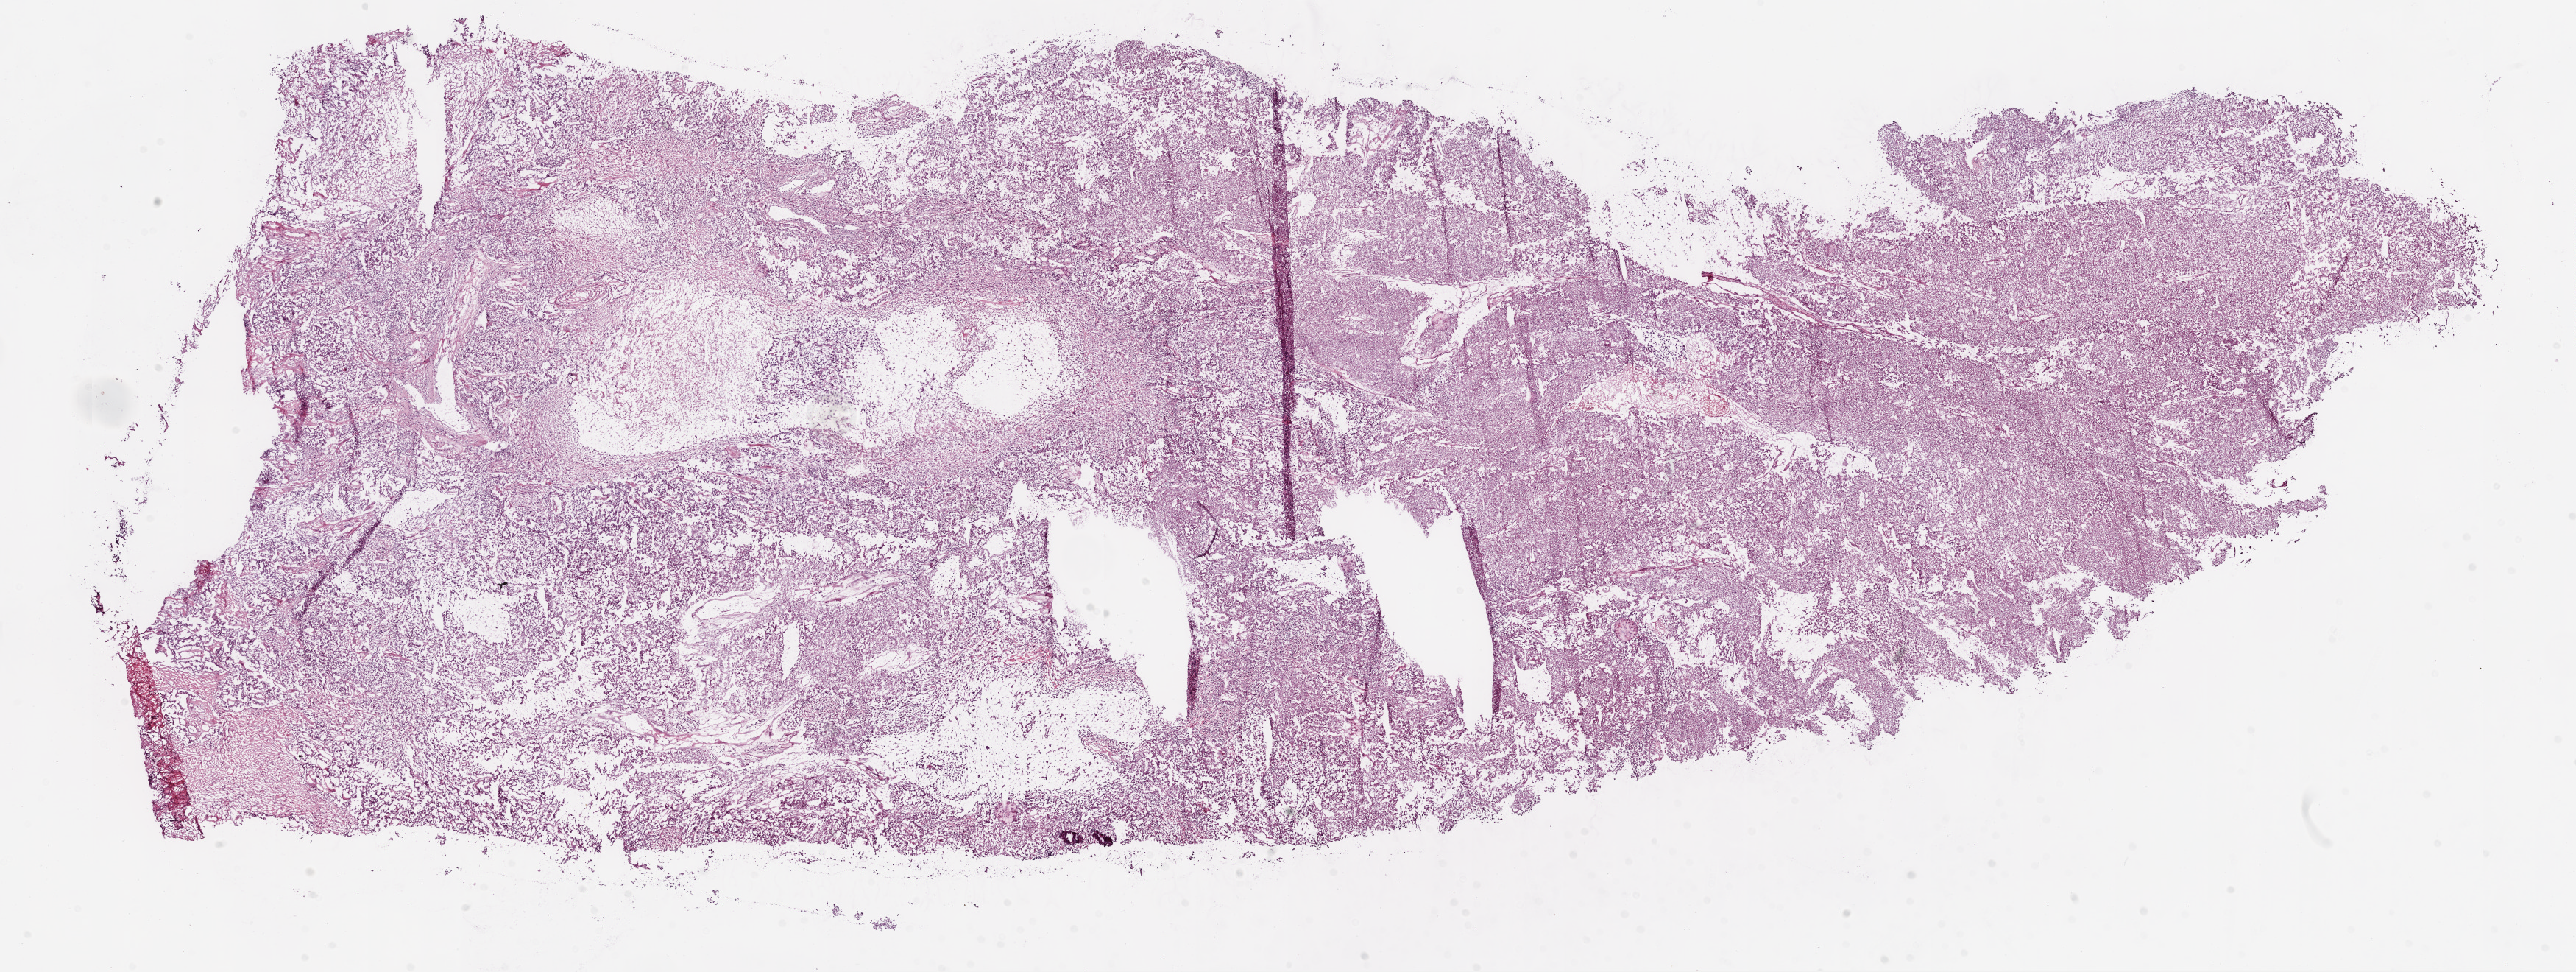
Digitized H&E tissue section (whole slide), low-resolution overview of the scanned area, about 28.1 x 10.6 mm (acquisition: 20x scan). Frozen section from the bottom of the tissue portion. Kidney, primary tumour sample. Male, age 74 years at initial diagnosis. Histologic grade: G4 (undifferentiated). Pathologist review of this section (percent, as recorded): tumour cells 95%, tumour nuclei 90%, normal cells 0%, stromal cells 5%, necrosis 5%.
- AJCC pathologic stage: IV
- histologic diagnosis: Clear cell adenocarcinoma, NOS